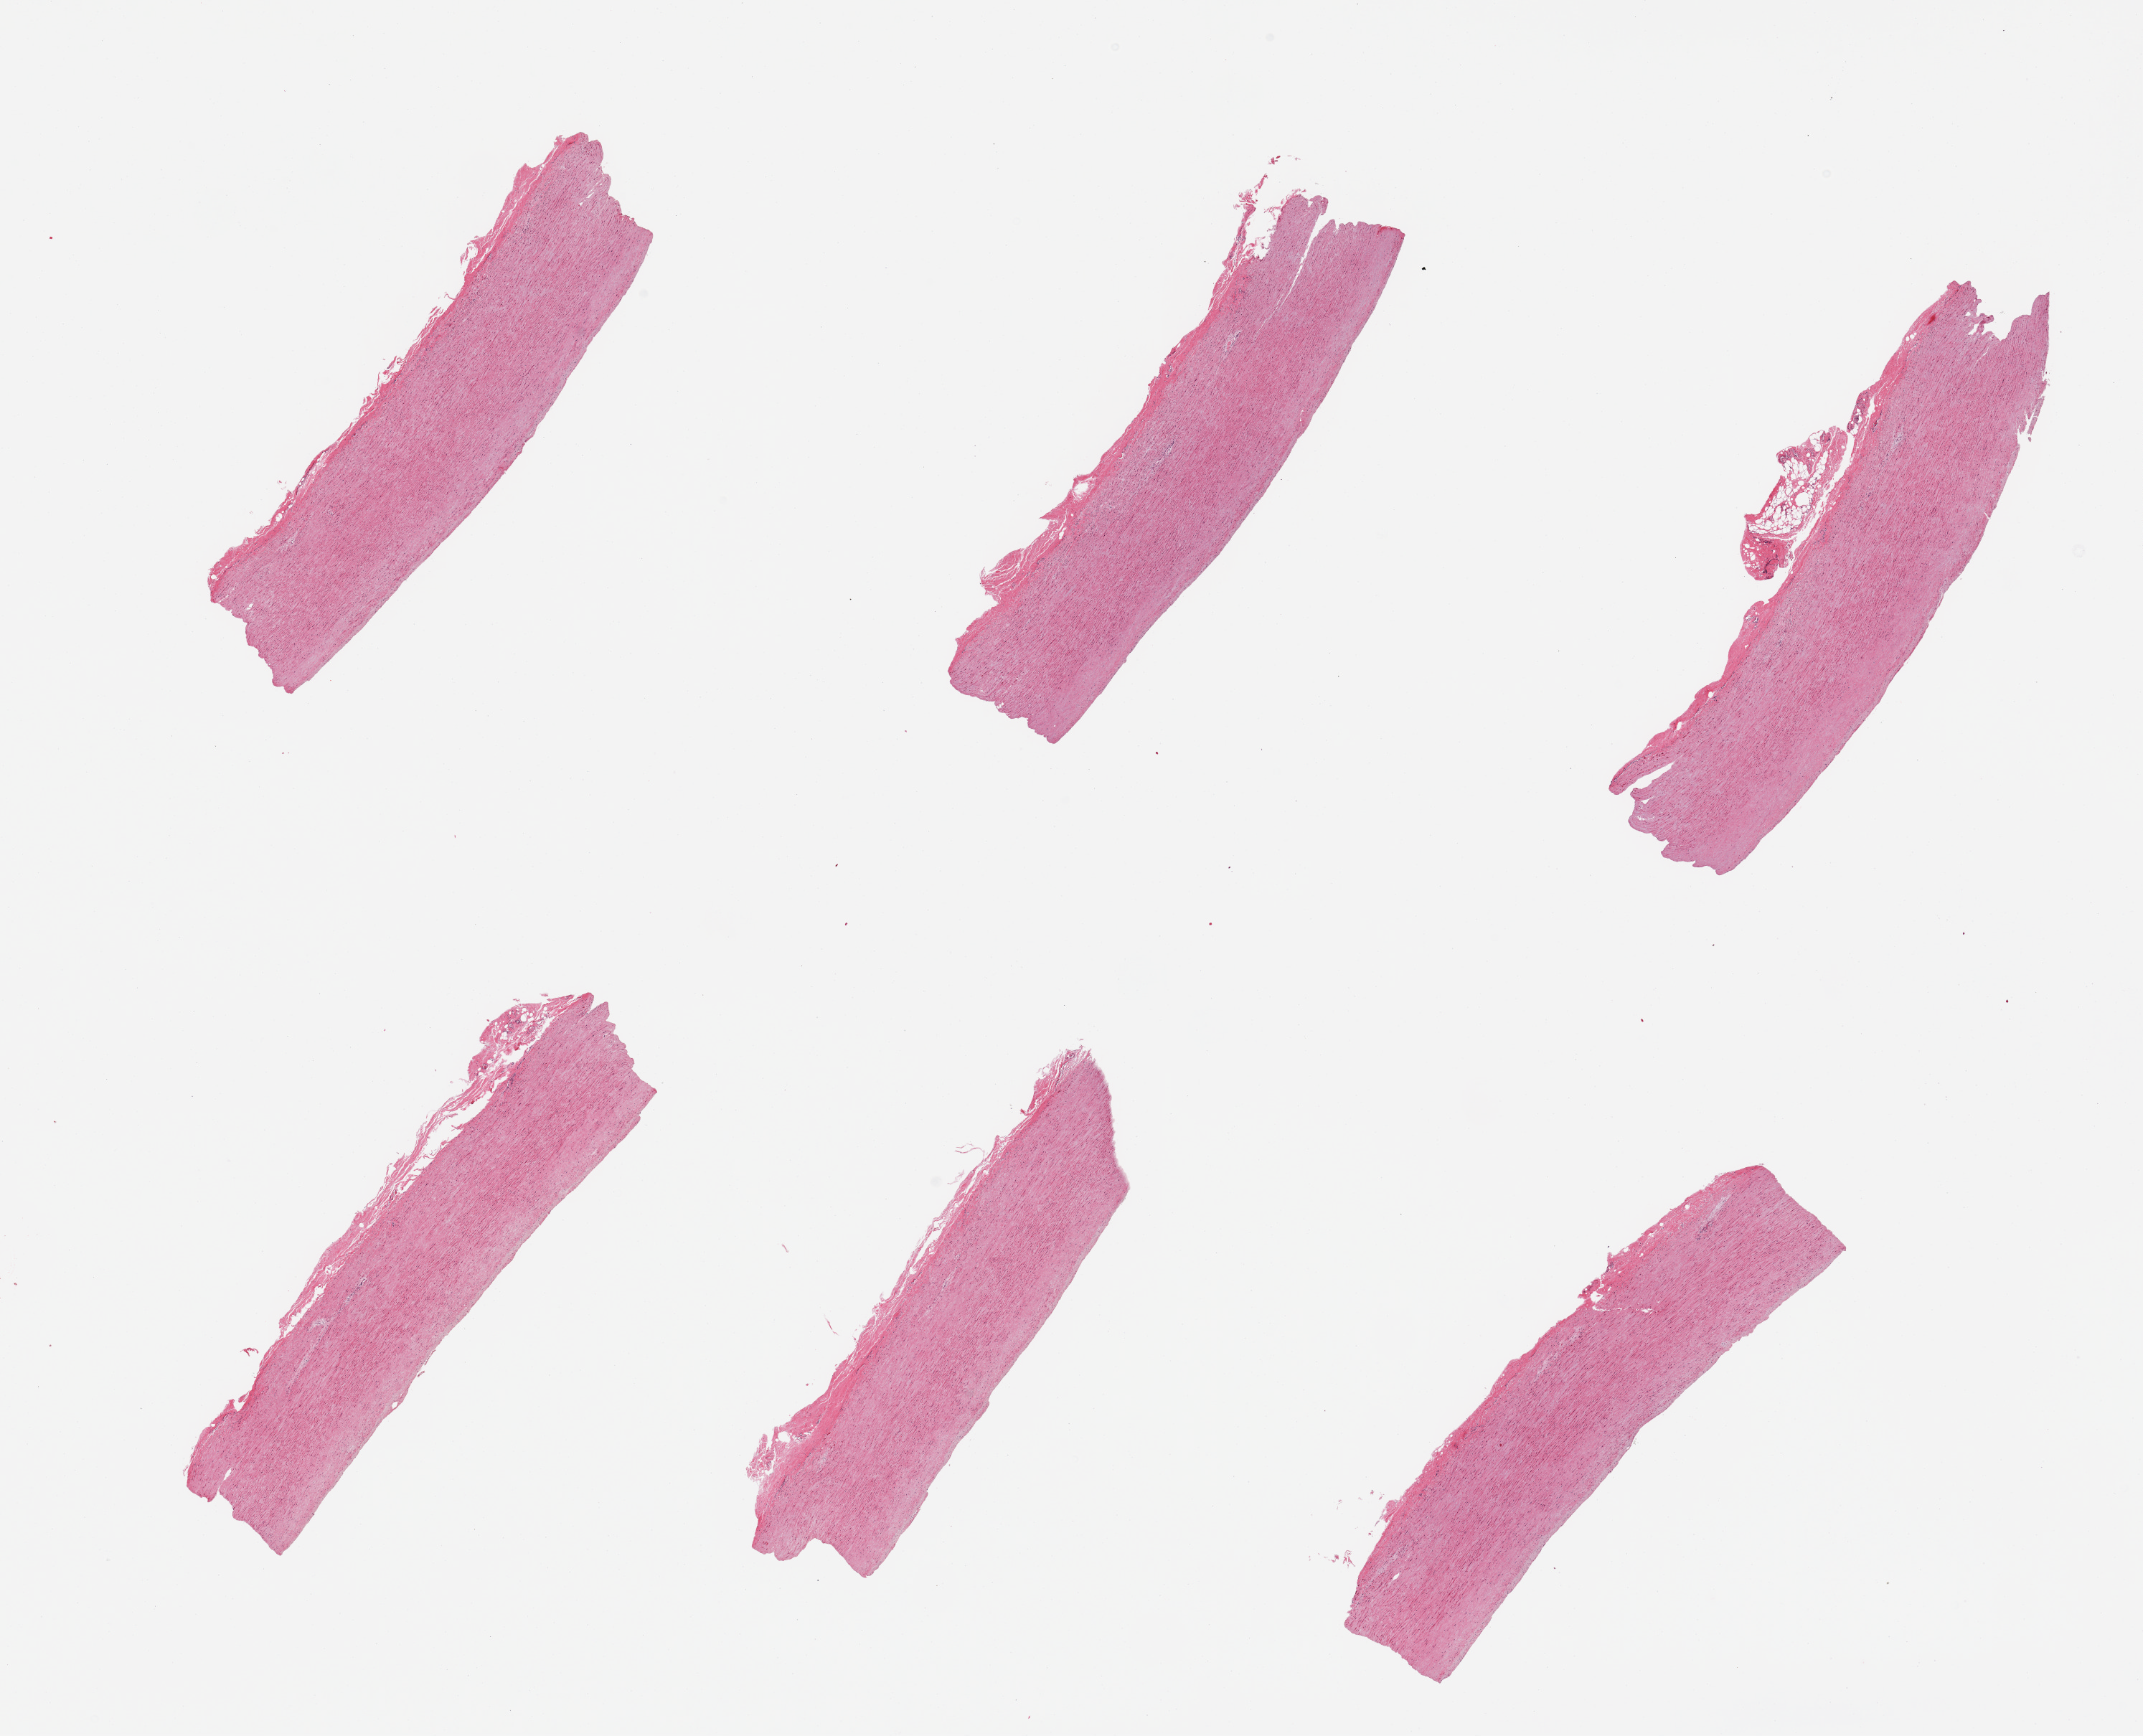
H&E whole-slide image, brightfield — whole scanned area (about 23.6 x 19.1 mm, from a 20x scan) shown as a low-resolution overview, PAXgene-fixed paraffin-embedded (PFPE) section, sampled site (target tissue): aorta, tissue donor sample. Donor: female.
• pathologist's review note for this sample: 6 pieces